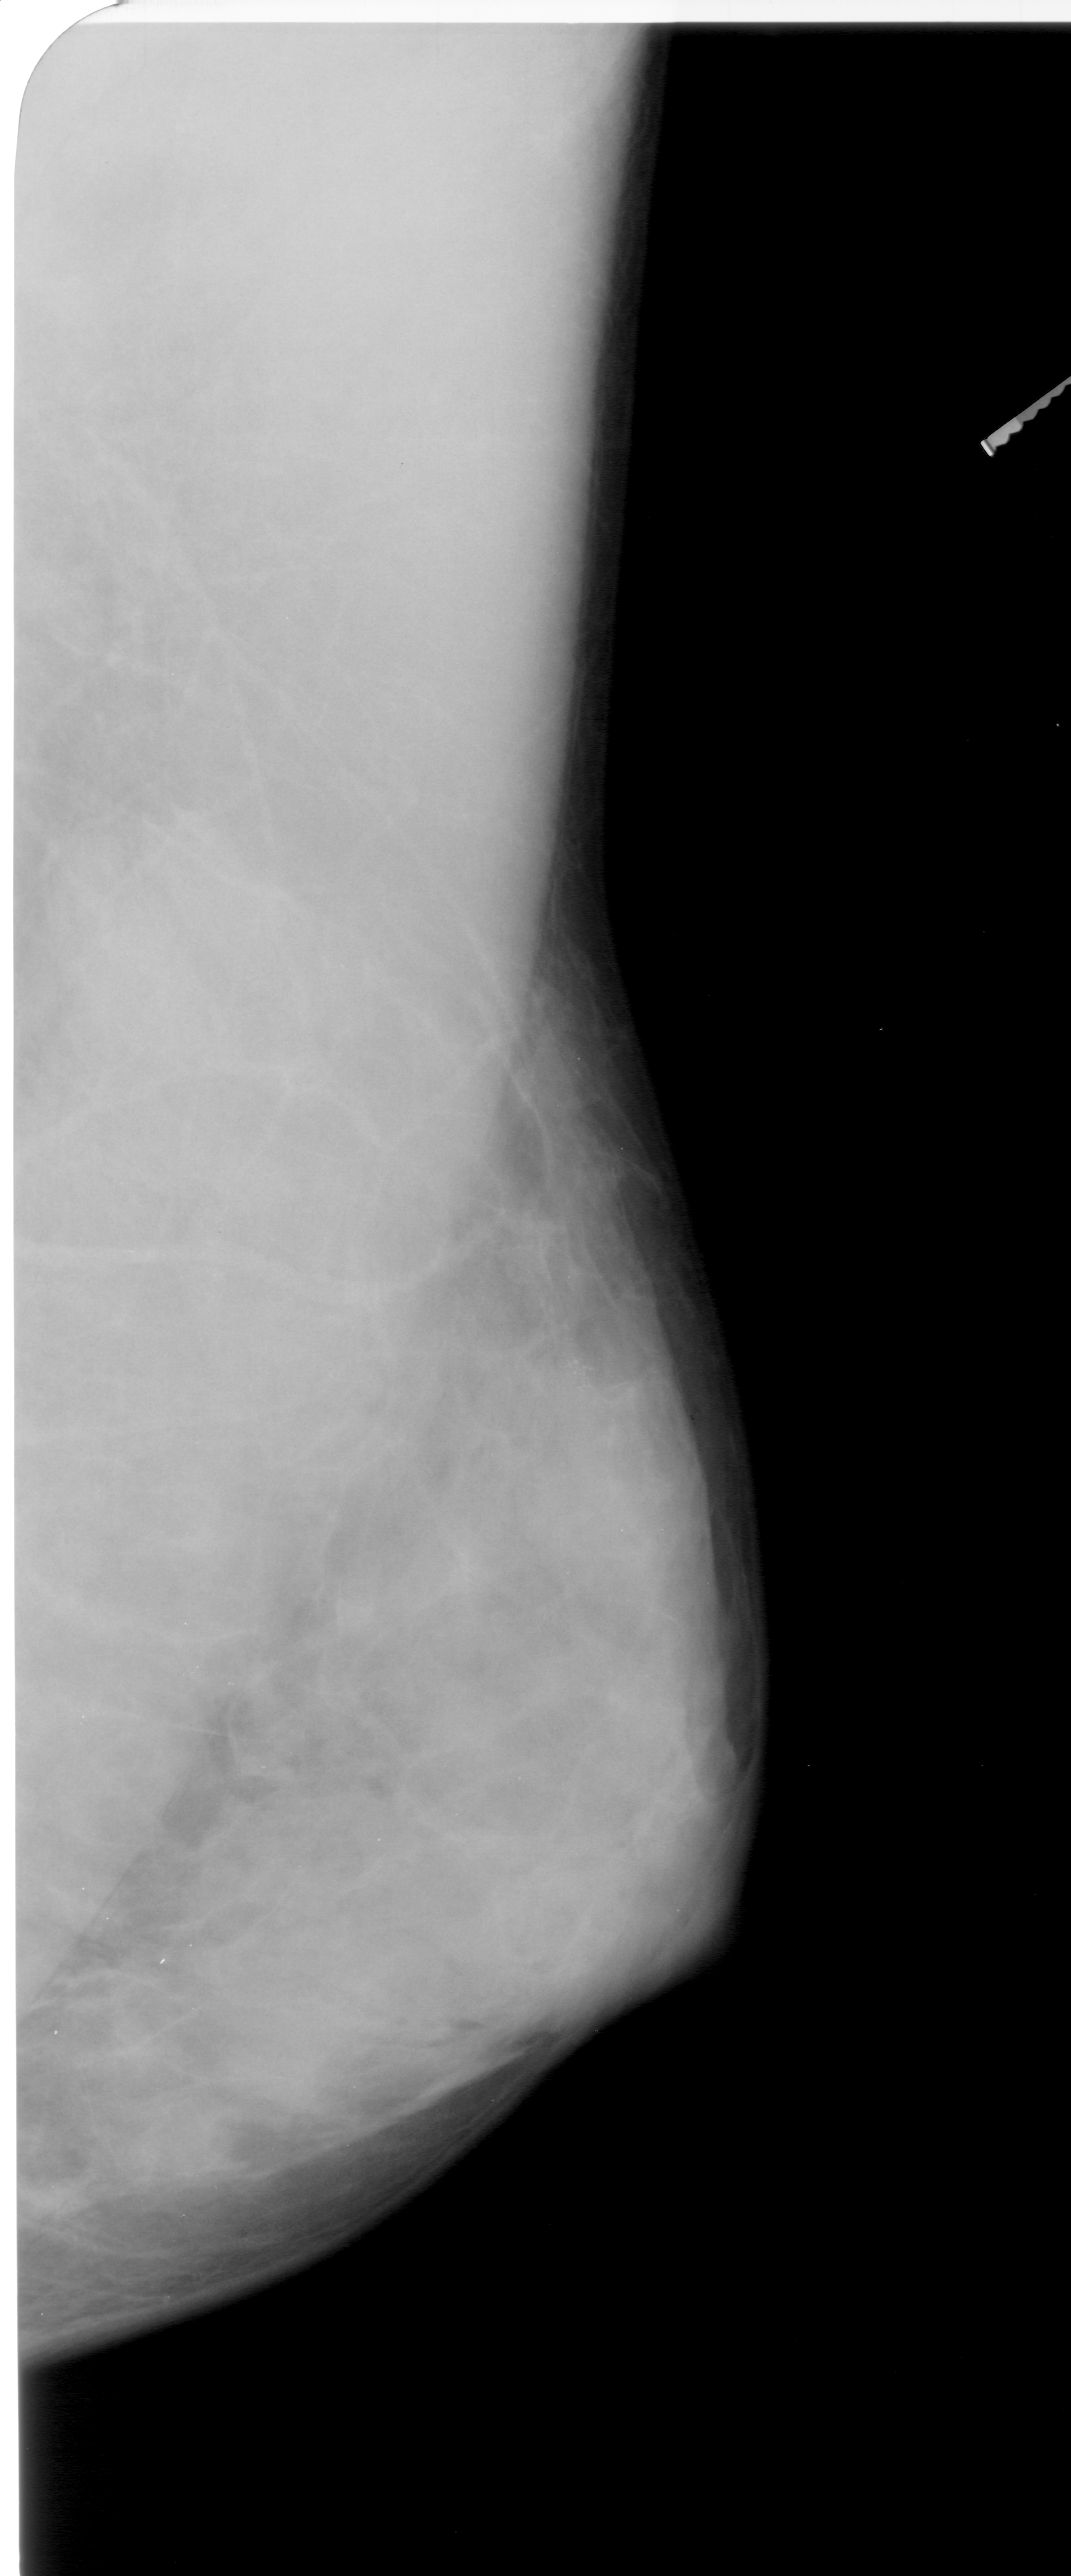
Scanned film-screen mammogram; right breast; mediolateral oblique (MLO) view; breast composition: extremely dense (BI-RADS density category 4 of 4).
Radiologist-marked abnormalities on this image: calcifications, morphology pleomorphic, distribution clustered; BI-RADS assessment category 4; subtlety rating 2 on a 1 (subtle) to 5 (obvious) scale; pathology (as recorded): benign.